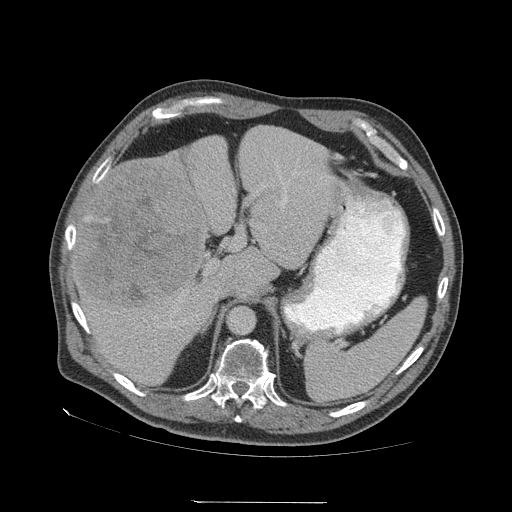
Contrast-enhanced abdominal CT (liver protocol), one axial slice; slice 41 of 83 in the series (ordered by position); reconstruction kernel STANDARD; soft-tissue window (W 400 / L 40 HU); 2.5 mm slice thickness; 512 × 512 image matrix, field of view 460 × 460 mm. From the clinical record (not read from this slice): diagnosis: hepatocellular carcinoma (patient treated with transarterial chemoembolisation; whether this scan precedes or follows treatment is not stated here); TNM stage (as recorded): Stage-I; Child-Pugh class: A.
Outlined on this slice (semi-automatically segmented with operator editing):
- liver parenchyma outside the tumour (the mass and vessels are separate outlines, so this box may not span the whole liver): bounding box <70,126,338,384> (left, top, right, bottom; pixels)
- mass: <76,161,206,310>
- liver vessels: <84,183,287,332>